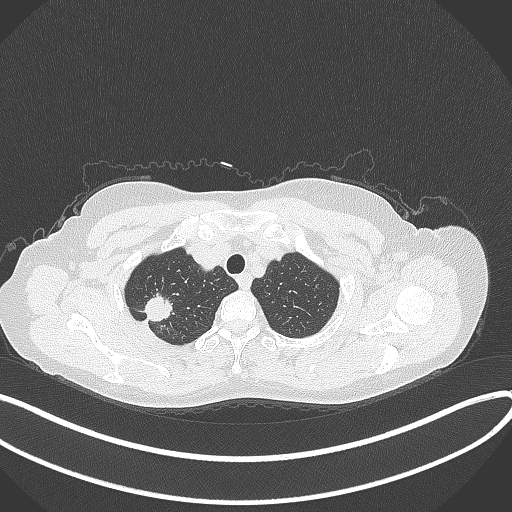
Chest CT, one axial slice; reconstruction kernel B70f; lung window (W 1500 / L -600 HU); 1 mm slice thickness; 512 × 512 image matrix. Female patient, age 50 years. Case-level facts recorded for this patient, not image findings: clinical TNM (as recorded): T1c N0 M0.
Annotated regions visible in this slice (rectangle marked by the reading radiologist):
- lung tumour (recorded histology: adenocarcinoma): bounding box <140,293,177,321> (left, top, right, bottom; pixels)